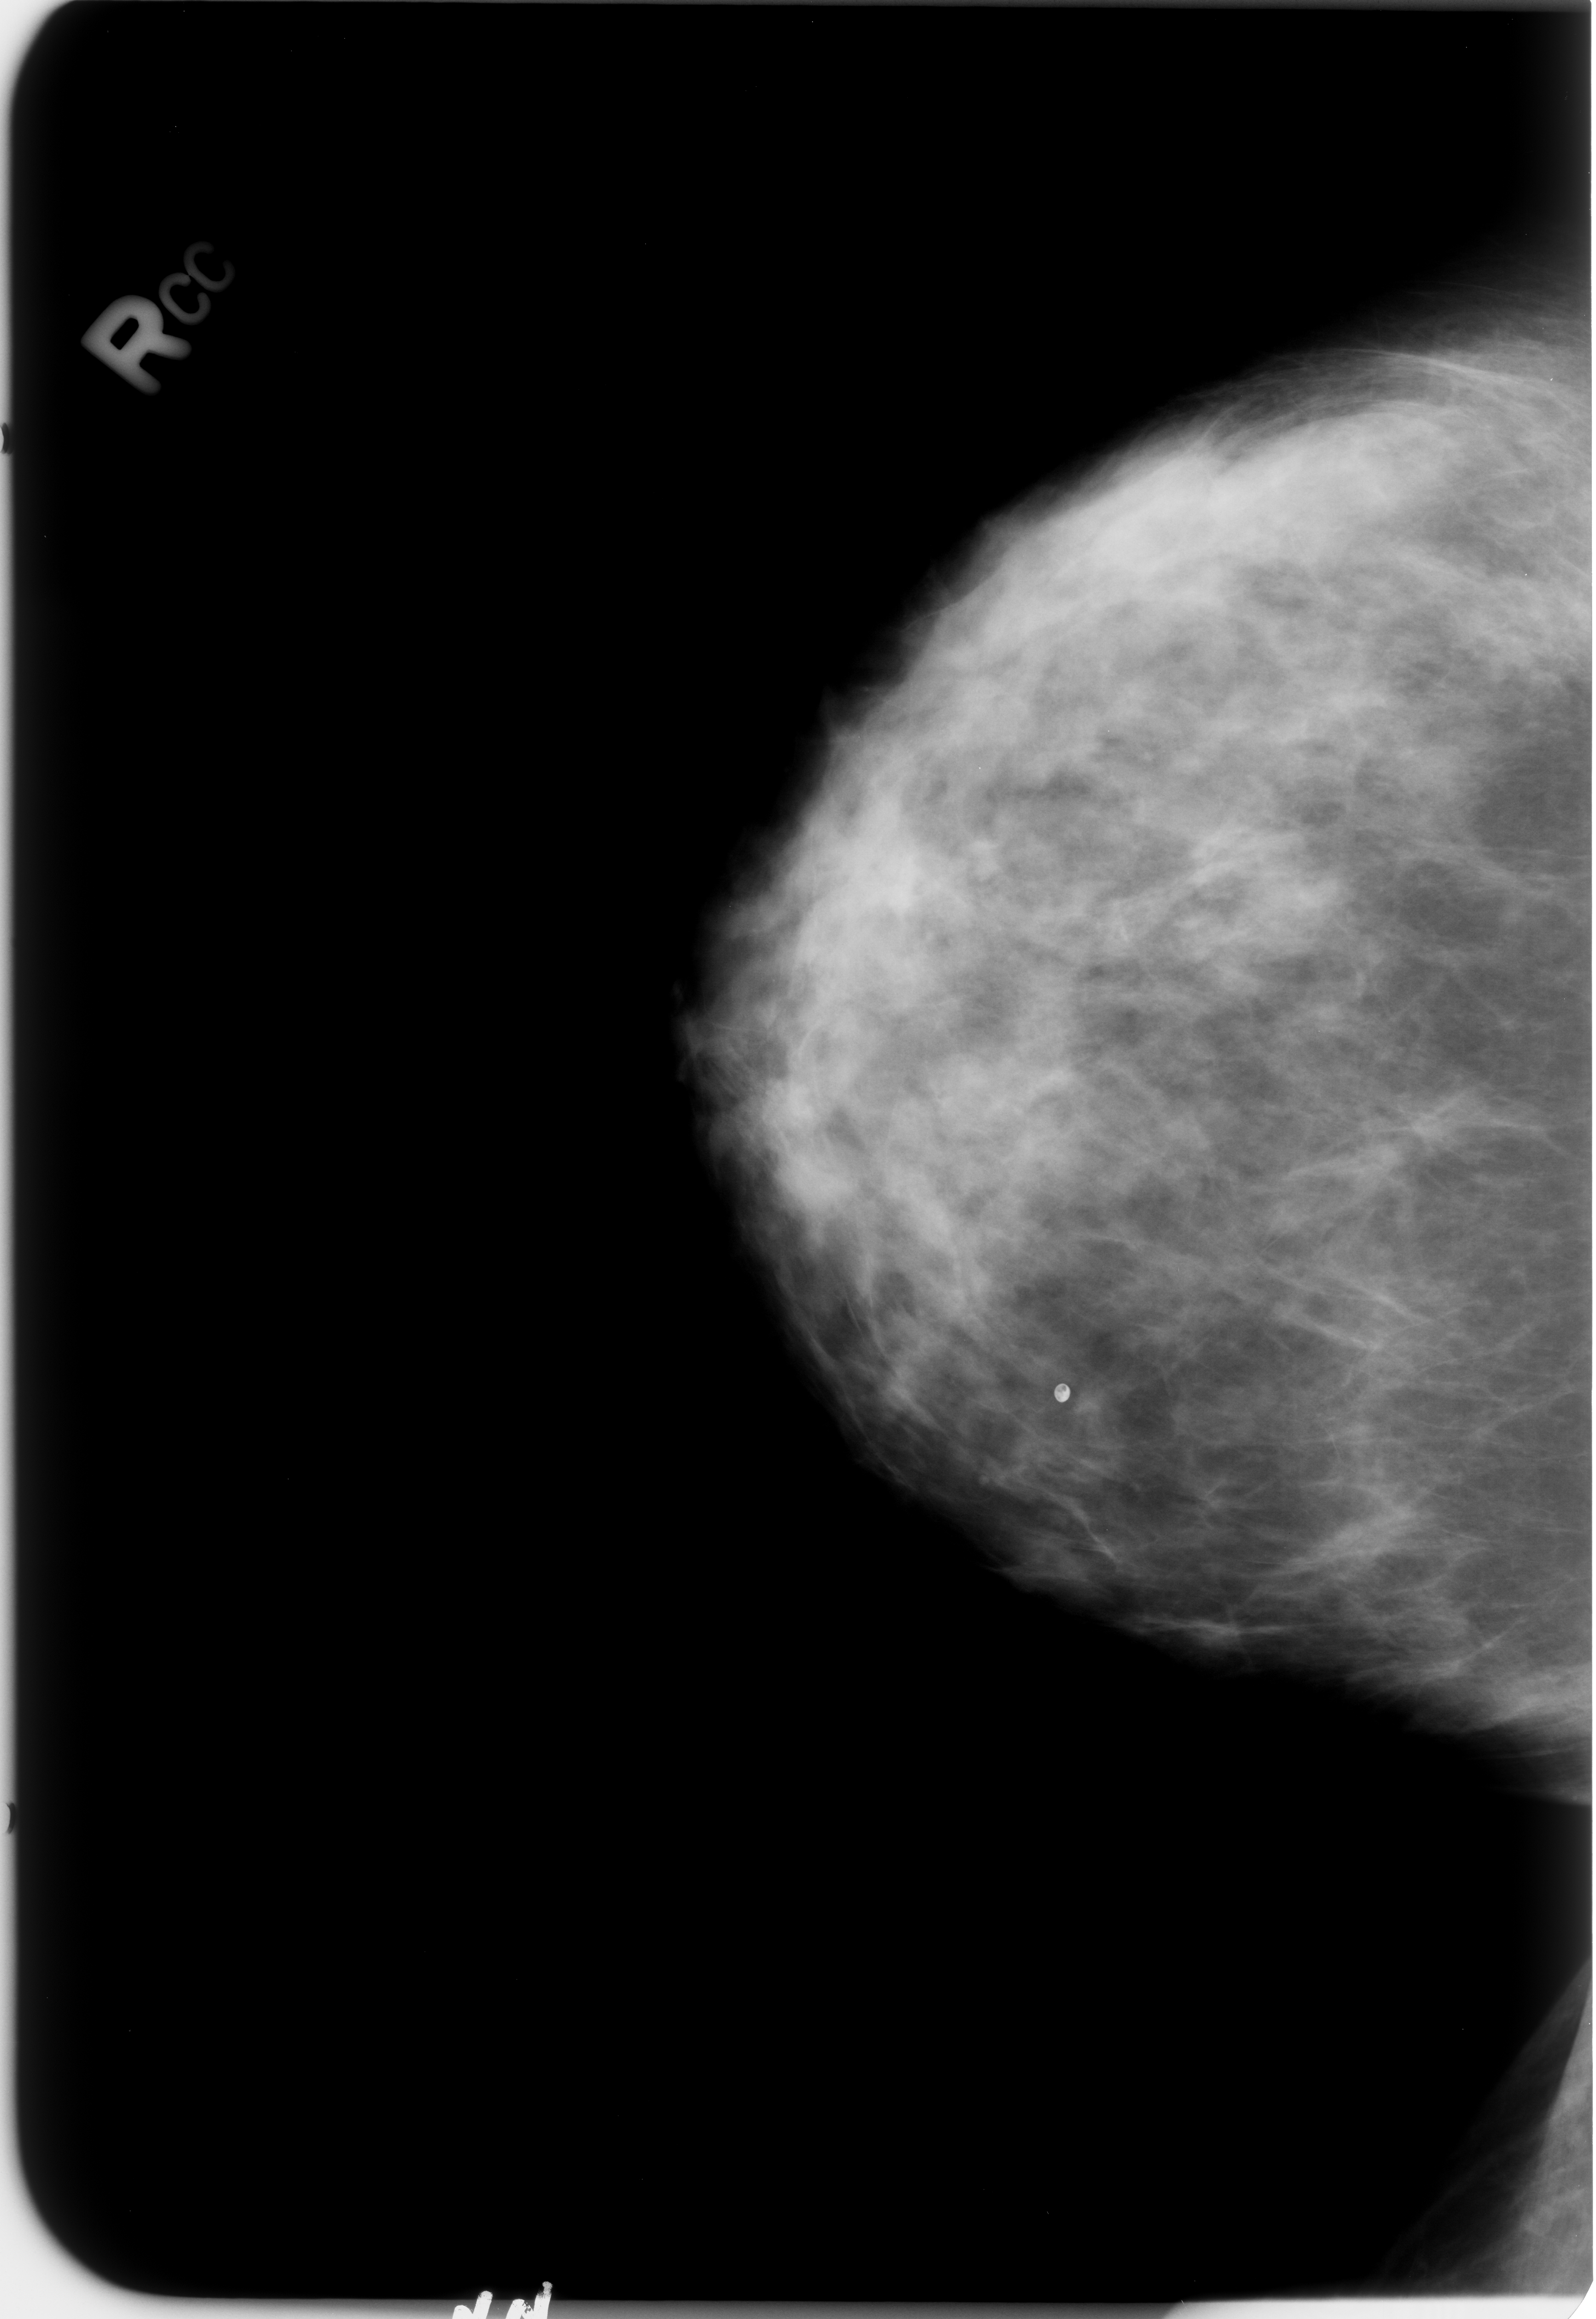
Digitized screen-film mammogram. Right breast. CC view. Breast composition: heterogeneously dense (BI-RADS density category 3 of 4). 1596 × 2319 image matrix.
Expert-marked regions of interest on this image (one box per marked abnormality):
- mass, shape oval, margins circumscribed / obscured; BI-RADS assessment category 3; pathology (as recorded): benign: bounding box <1208,382,1443,530> (left, top, right, bottom; pixels)